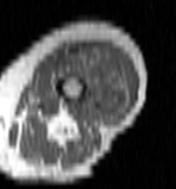
MRI of an extremity soft-tissue mass, one axial slice; slice 36 of 100 in the series (ordered by position); MR volume resampled by the dataset authors to the PET/CT grid (not the native acquisition matrix); 3.27 mm slice thickness; 176 × 189 image matrix. Female patient. From the clinical record (not read from this slice): histological type: undifferentiated – high grade; grade: high; site of the primary tumour: left thigh.
Annotated regions visible in this slice (expert contour drawn on MRI and transferred to this co-registered scan by the dataset authors):
- gross tumour volume including surrounding oedema: bounding box (x1, y1, x2, y2) in pixels: (62, 48, 127, 120)
- gross tumour volume (mass): (96, 59, 122, 120)